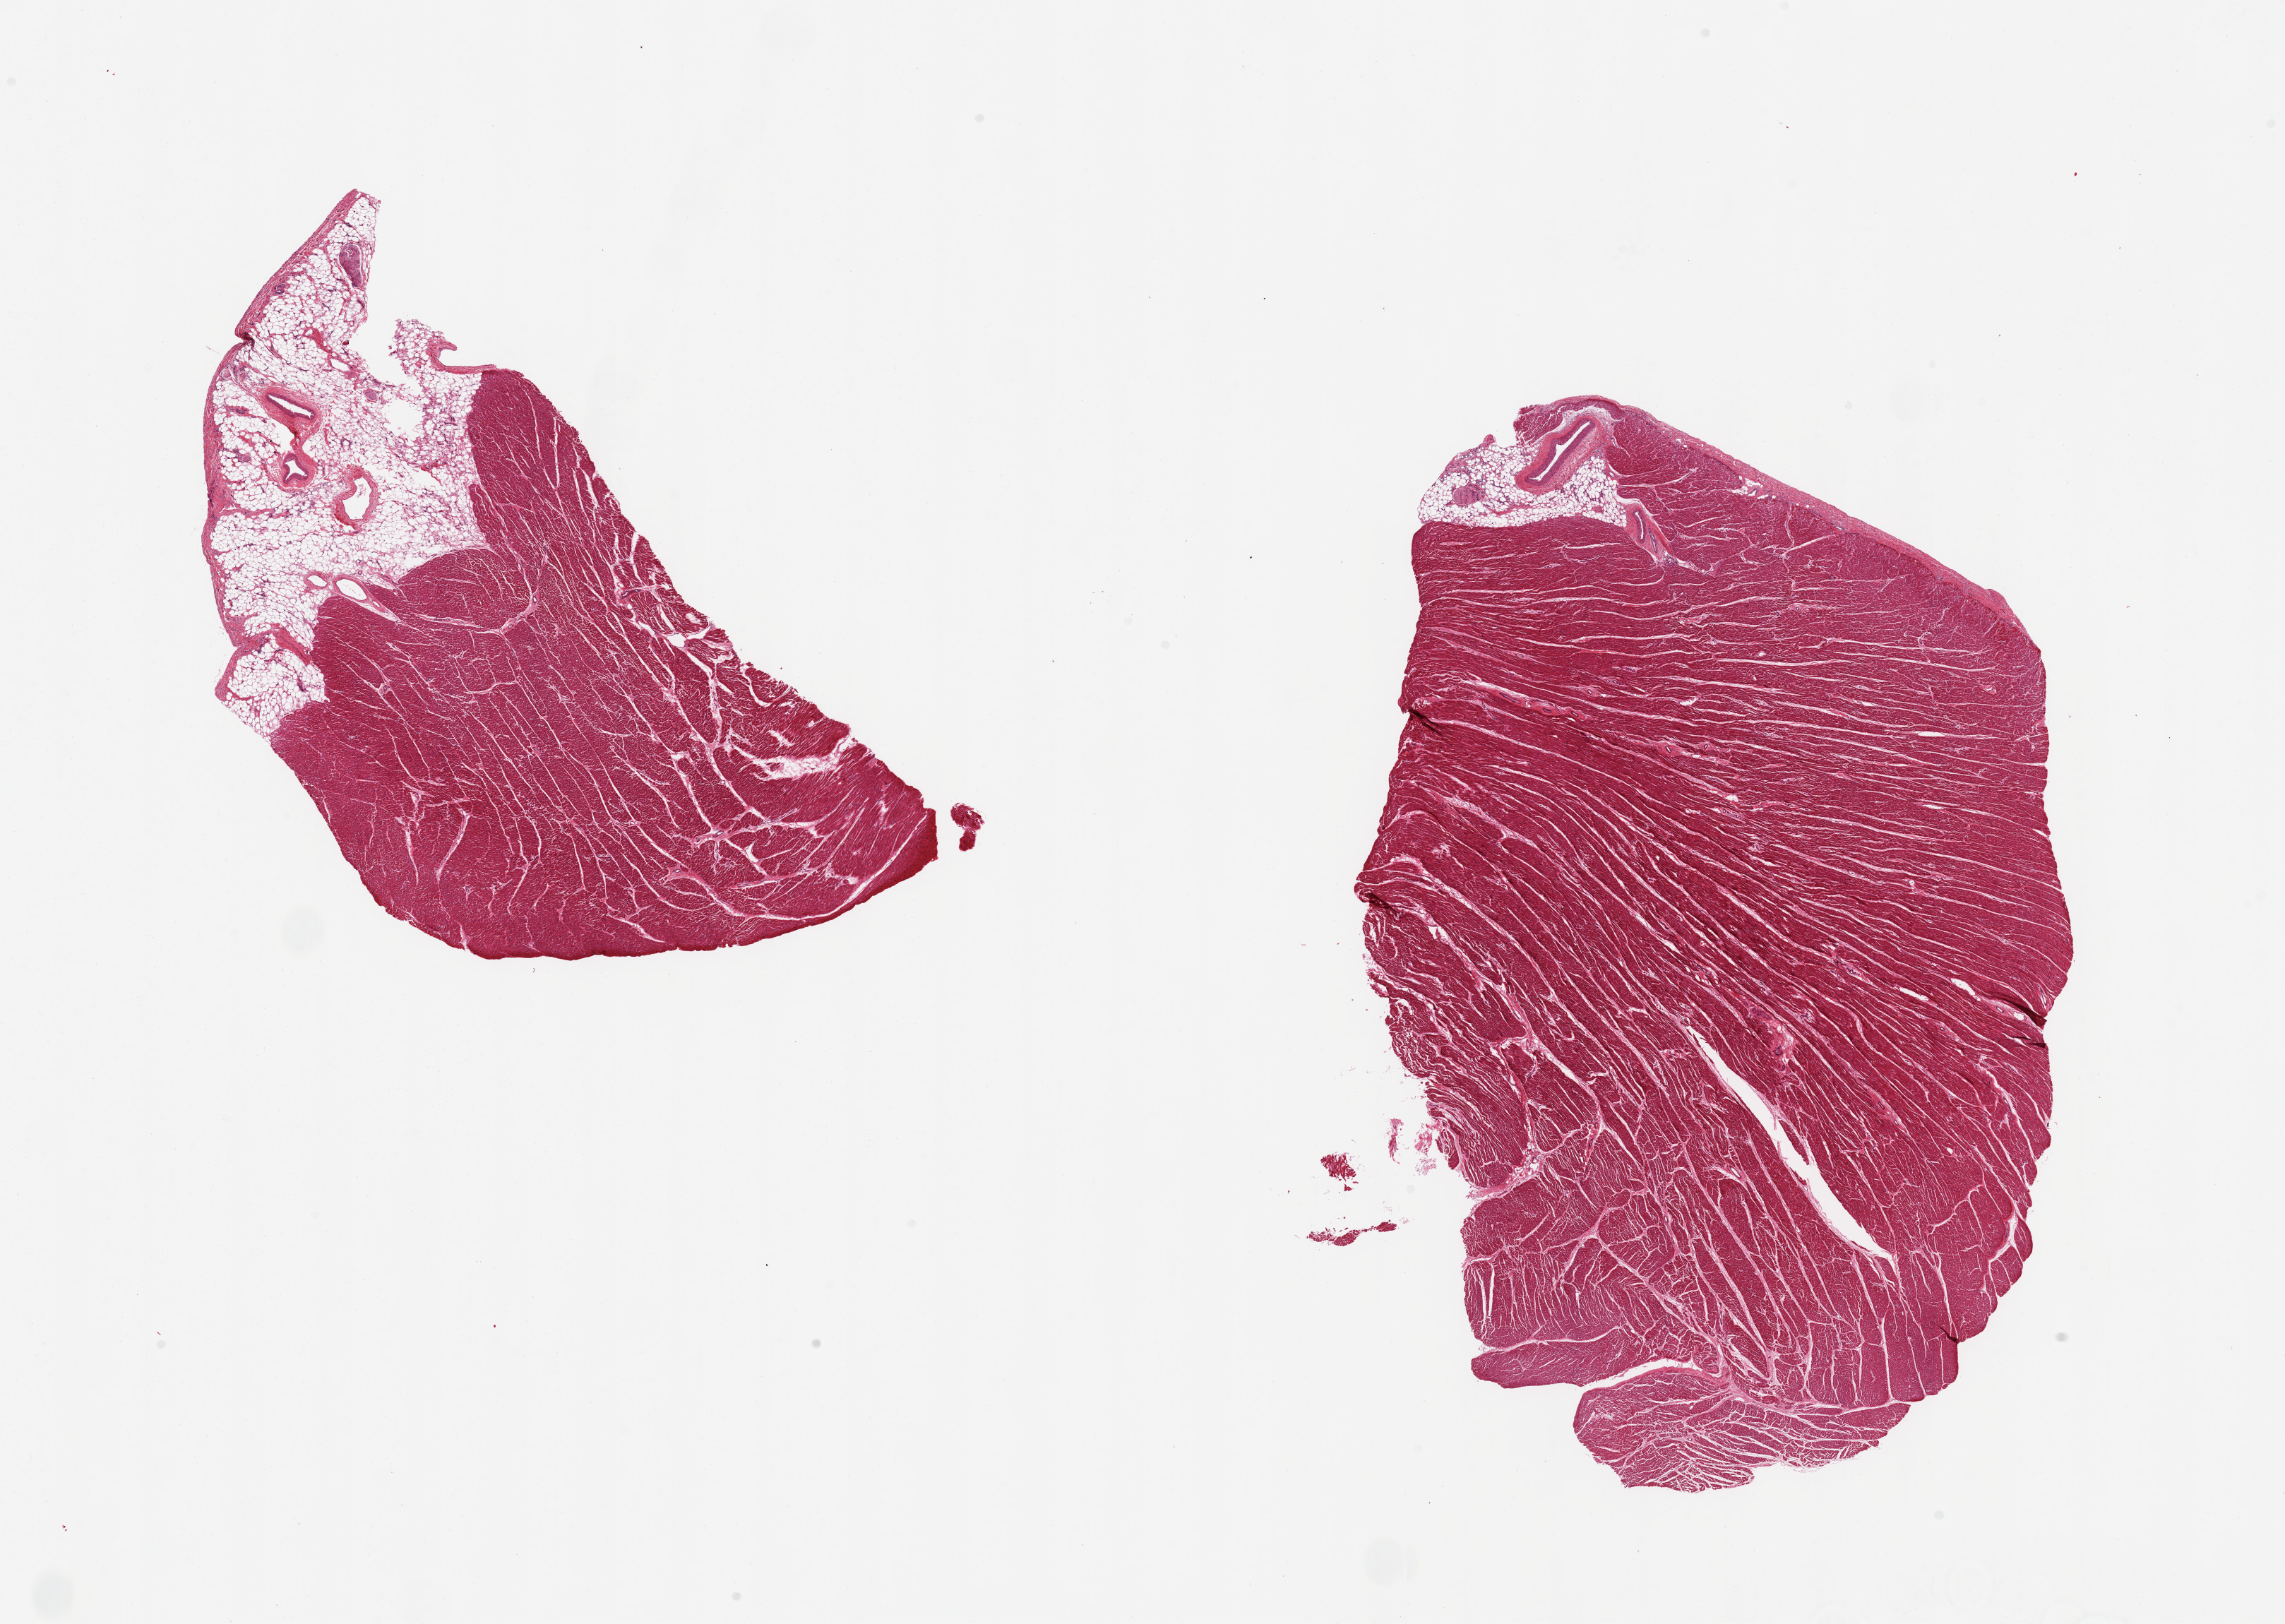
H&E whole-slide image, brightfield, low-resolution overview of the scanned area, about 25.6 x 18.2 mm (from a 20x scan); PAXgene-fixed paraffin-embedded (PFPE) section; sampled site (target tissue): heart; tissue donor sample. Donor: female.
- review note (as recorded): 2 pieces; 1 piece contains 30% external fat